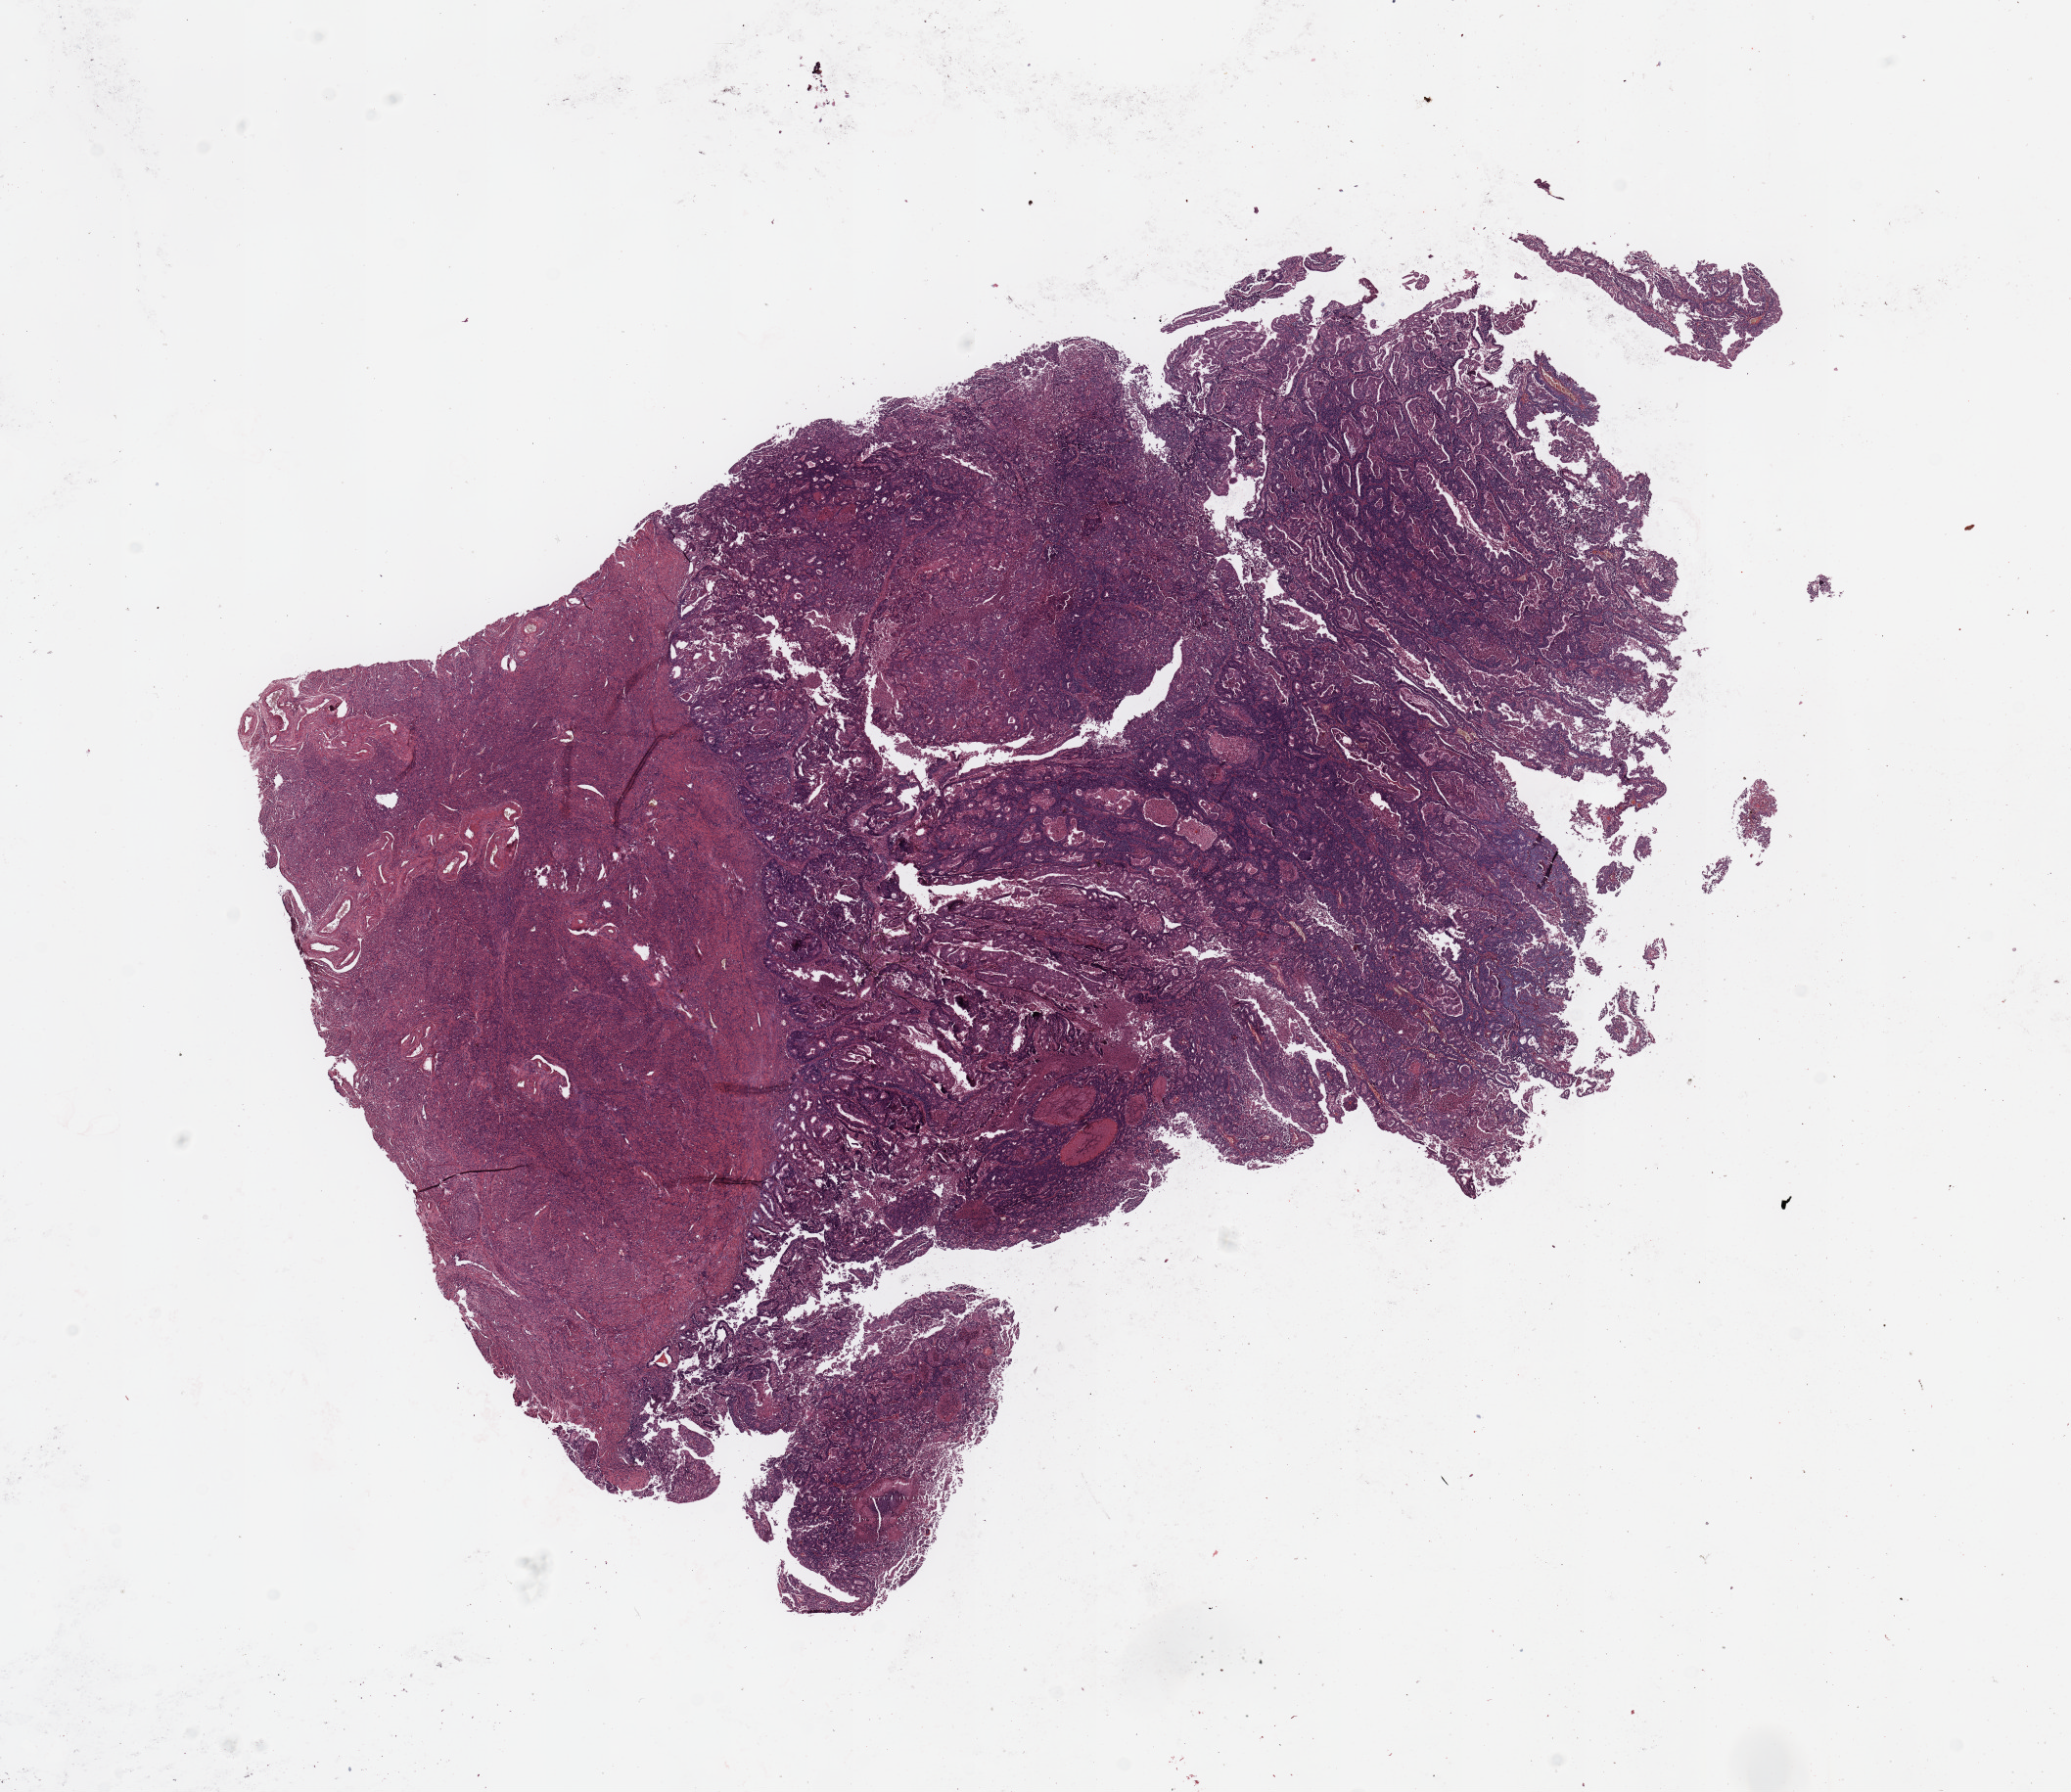
H&E-stained whole-slide image, shown as a low-resolution overview of the whole scanned area (about 16.7 x 14.5 mm), uterus, tumour tissue. Female, 77 y/o.
Histologic diagnosis: Endometrioid adenocarcinoma, NOS.